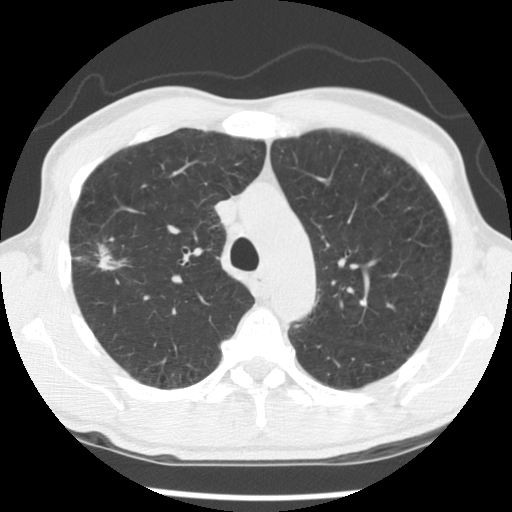
Axial slice from a low-dose chest CT screening exam. Second screening round (one year after baseline). Lung window (W 1500 / L -600 HU). 2.5 mm slice thickness. Male participant, aged 56 years at enrolment. Current smoker at enrolment.
Lesion marked by an expert reader, bounding box (x1, y1, x2, y2) in pixels: (57, 230, 142, 297). Screening reader's record for this exam (one nodule recorded; not confirmed to be the boxed lesion): non-calcified nodule or mass ≥4 mm, right upper lobe, 30 × 18 mm, spiculated (stellate) margins, mixed attenuation, pre-existing on the prior screen: yes; interval growth: yes. Official screen result: positive, other.